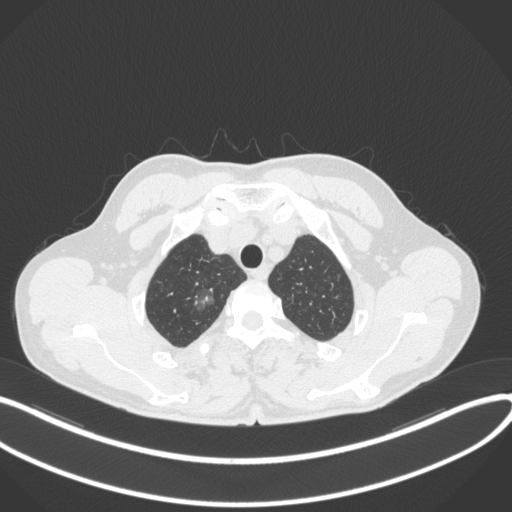
Chest CT, one axial slice. Position 331 of 407 along the scan axis. 120 kVp. Lung window (W 1500 / L -600 HU). 1 mm slice thickness. 512 × 512 image matrix, field of view 400 × 400 mm. Patient: male, 58 years. Case-level facts recorded for this patient, not image findings: clinical TNM (as recorded): T1c N0 M0; histopathological grade: G1-2.
Annotated regions visible in this slice (rectangle marked by the reading radiologist):
- lung tumour (recorded histology: adenocarcinoma): bounding box (x1, y1, x2, y2) in pixels: (193, 282, 219, 318)